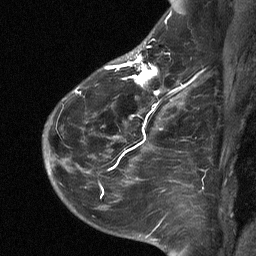
Breast MRI (dynamic contrast-enhanced), one sagittal slice. Slice 45 of 64 in the series (ordered by position). Dynamic contrast-enhanced study with each time point stored as its own series, time point 2 of 3 at this slice position (early post-contrast, ordered by acquisition time). 1.5 T. TE 4.8 ms, TR 27 ms. 2 mm slice thickness. 256 × 256 image matrix, field of view 180 × 180 mm. Female patient, age 51 years. From the clinical record (not read from this slice): setting: breast cancer imaged before/during neoadjuvant chemotherapy; receptor status: HR-positive, HER2-negative.
Outlined on this slice (semi-automatically segmented with operator editing):
- analysis volume of interest (the breast-tissue region the enhancement analysis was run in; not a lesion): bounding box (x1, y1, x2, y2) in pixels: (72, 34, 182, 118)
- tumour enhancement mask (voxels above the 90 % enhancement threshold inside the analysis volume of interest): (76, 46, 176, 118)